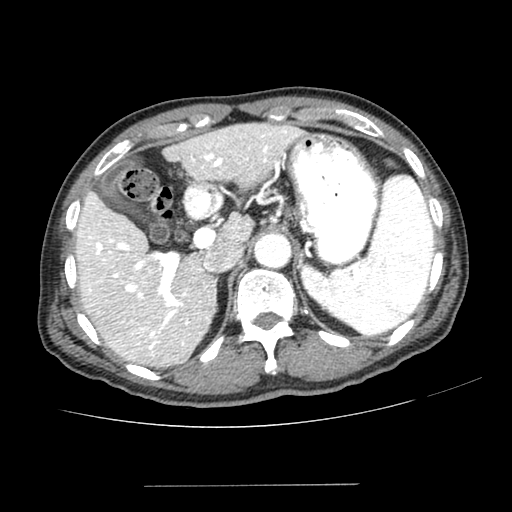
Contrast-enhanced abdominal CT (liver protocol), one axial slice. Position 158 of 187 along the scan axis. Reconstruction kernel SOFT. One of 2 acquisitions stored at this slice position. Soft-tissue window (W 400 / L 40 HU). 2.5 mm slice thickness. 512 × 512 image matrix, field of view 360 × 360 mm. From the clinical record (not read from this slice): diagnosis: hepatocellular carcinoma (patient treated with transarterial chemoembolisation; whether this scan precedes or follows treatment is not stated here); TNM stage (as recorded): Stage-I; Child-Pugh class: A; tumour differentiation: poorly differentiated; tumour nodularity: uninodular.
Annotated regions visible in this slice (semi-automatically segmented with operator editing):
- liver parenchyma outside the tumour (the mass and vessels are separate outlines, so this box may not span the whole liver): box from (x=76, y=124) to (x=300, y=366) px
- liver vessels: (x=88, y=130)–(x=289, y=356)